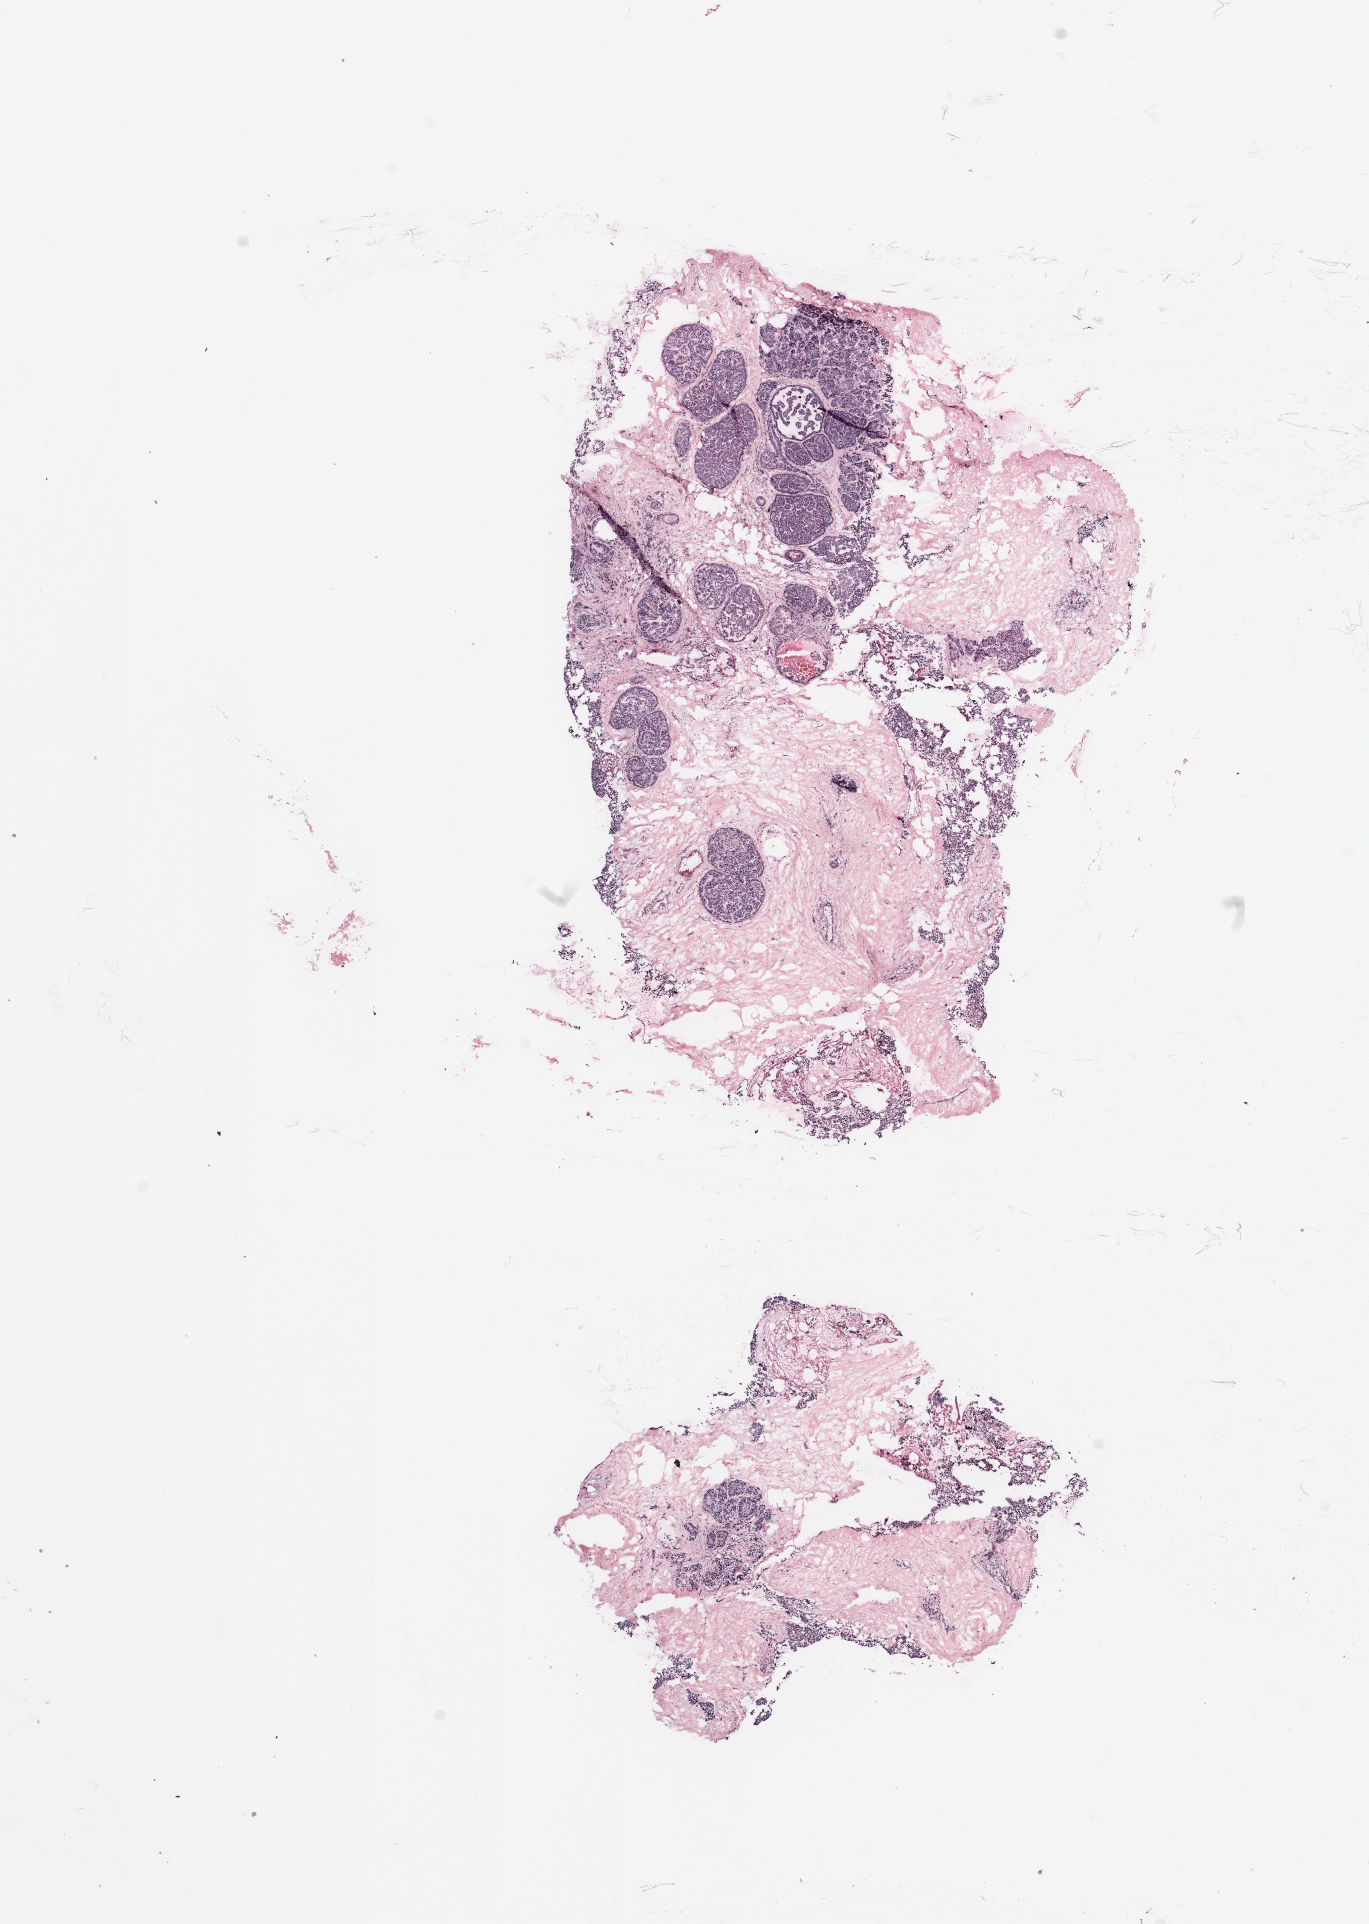
Hematoxylin and eosin (H&E) stained whole-slide image — low-resolution overview of the scanned area, about 10.8 x 15.2 mm. Patient: female, age 52 years.
Specimen: breast, tumour tissue.